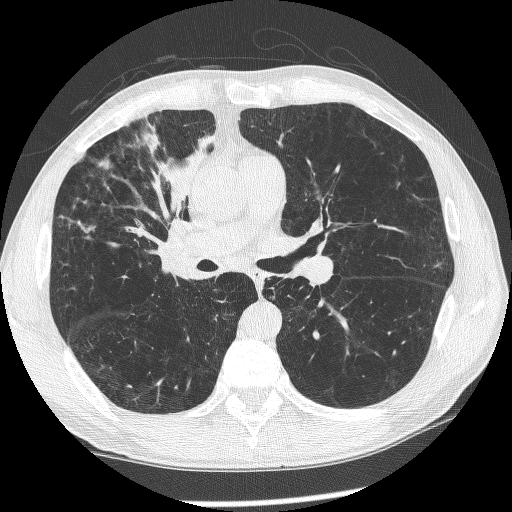
Axial slice from a low-dose chest CT screening exam. Baseline screening round. Lung window (W 1500 / L -600 HU). Slice 138 of 266 in the series. Male, age 60 years at enrolment.
Expert reader's lesion annotation, box from (x=146, y=180) to (x=217, y=274) px. The exam's reader record, not a measurement of the box and not confirmed to be the same lesion: non-calcified nodule or mass ≥4 mm, right upper lobe, 12 × 8 mm, spiculated (stellate) margins, mixed attenuation. Official screen result: positive, change unspecified: nodule(s) >= 4 mm or enlarging nodule(s), mass(es), or other non-specific abnormalities suspicious for lung cancer.